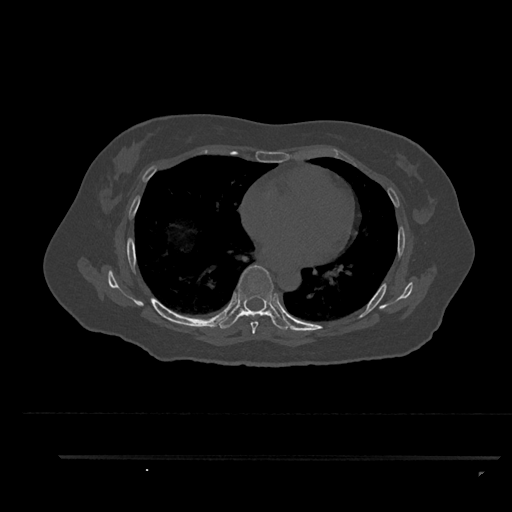
CT including the spine, one axial slice. Position 525 of 797 along the scan axis. Reconstruction kernel Br40s/3. 120 kVp. Bone window (W 1800 / L 400 HU). 512 × 512 image matrix, field of view 408 × 408 mm. Patient: female, 44 years. Case-level facts recorded for this patient, not image findings: primary cancer: renal; vertebrae with lytic lesions (as recorded): L1.
Structures marked on this image (semi-automatically segmented with operator editing):
- T6 vertebra: bounding box [x1, y1, x2, y2] px = [250, 314, 258, 334]
- T7 vertebra: [216, 265, 290, 330]